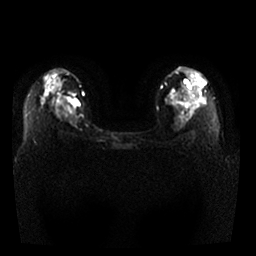
Breast MRI, one axial slice; position 22 of 29 along the scan axis; diffusion-weighted series; image 2 of 4 stored at this slice position (different b-values; order by instance number); 1.5 T; 4 mm slice thickness; 256 × 256 image matrix, field of view 340 × 340 mm. Female patient.
Structures marked on this image (outlined manually by an expert reader):
- tumour on diffusion-weighted imaging: bounding box (x1, y1, x2, y2) in pixels: (67, 98, 79, 107)